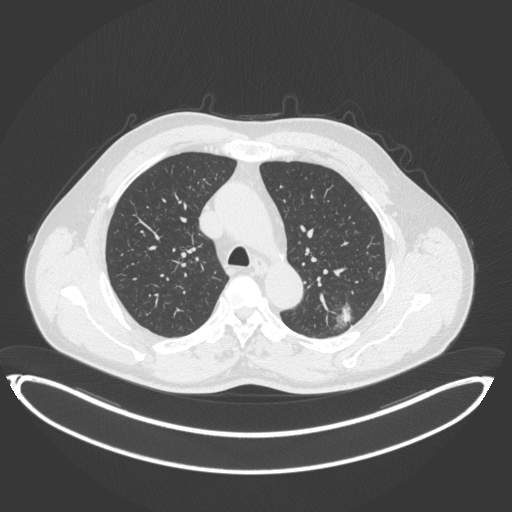
Chest CT, one axial slice. Position 255 of 399 along the scan axis. Reconstruction kernel B31f. 120 kVp. Lung window (W 1500 / L -600 HU). 1 mm slice thickness. 512 × 512 image matrix, field of view 469 × 469 mm. Male patient, age 58 years. Case-level facts recorded for this patient, not image findings: clinical TNM (as recorded): T1c N0 M0.
Structures marked on this image (rectangle marked by the reading radiologist):
- lung tumour (recorded histology: adenocarcinoma): bounding box <330,297,356,331> (left, top, right, bottom; pixels)